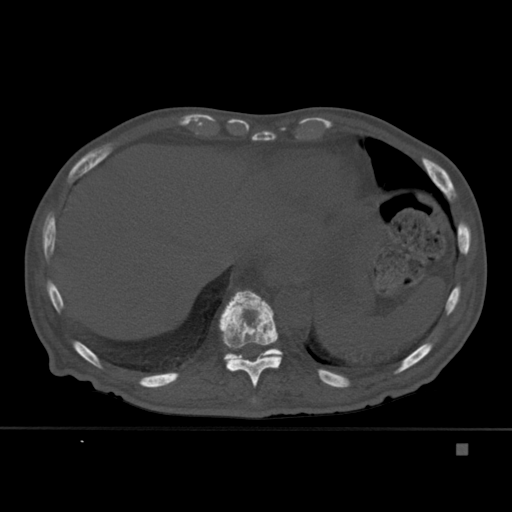
CT including the spine, one axial slice; position 230 of 451 along the scan axis; bone window (W 1800 / L 400 HU); 512 × 512 image matrix, field of view 378 × 378 mm. Male patient, age 75 years. Case-level facts recorded for this patient, not image findings: primary cancer: prostate.
Structures marked on this image (semi-automatic segmentation, software-assisted and operator-edited):
- T10 vertebra: bounding box (x1, y1, x2, y2) in pixels: (219, 290, 282, 388)
- T11 vertebra: (224, 348, 283, 361)
- T9 vertebra: (252, 398, 256, 403)